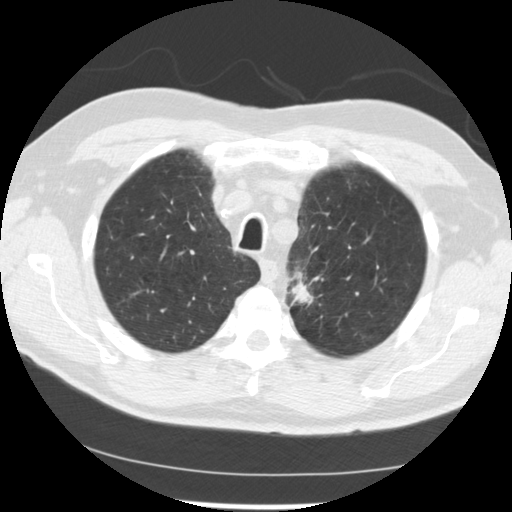
Axial slice from a low-dose chest CT screening exam, first (baseline) screen, lung window (W 1500 / L -600 HU), 2.5 mm slice thickness, standard (soft-tissue) reconstruction kernel (STANDARD), 512 × 512 image matrix, field of view 341 × 341 mm. Male participant, aged 71 years at enrolment.
Expert-annotated lung lesion, bounding box (x1, y1, x2, y2) in pixels: (275, 261, 335, 316). The screening reader recorded 2 non-calcified nodules or masses ≥4 mm on this exam (left upper lobe, left upper lobe); which of them this box marks is not recorded. Lung cancer was diagnosed 37 days after this screen: adenocarcinoma, NOS, left upper lobe, poorly differentiated (G3), stage IIIB (AJCC 6th edition), 25 mm at pathology.